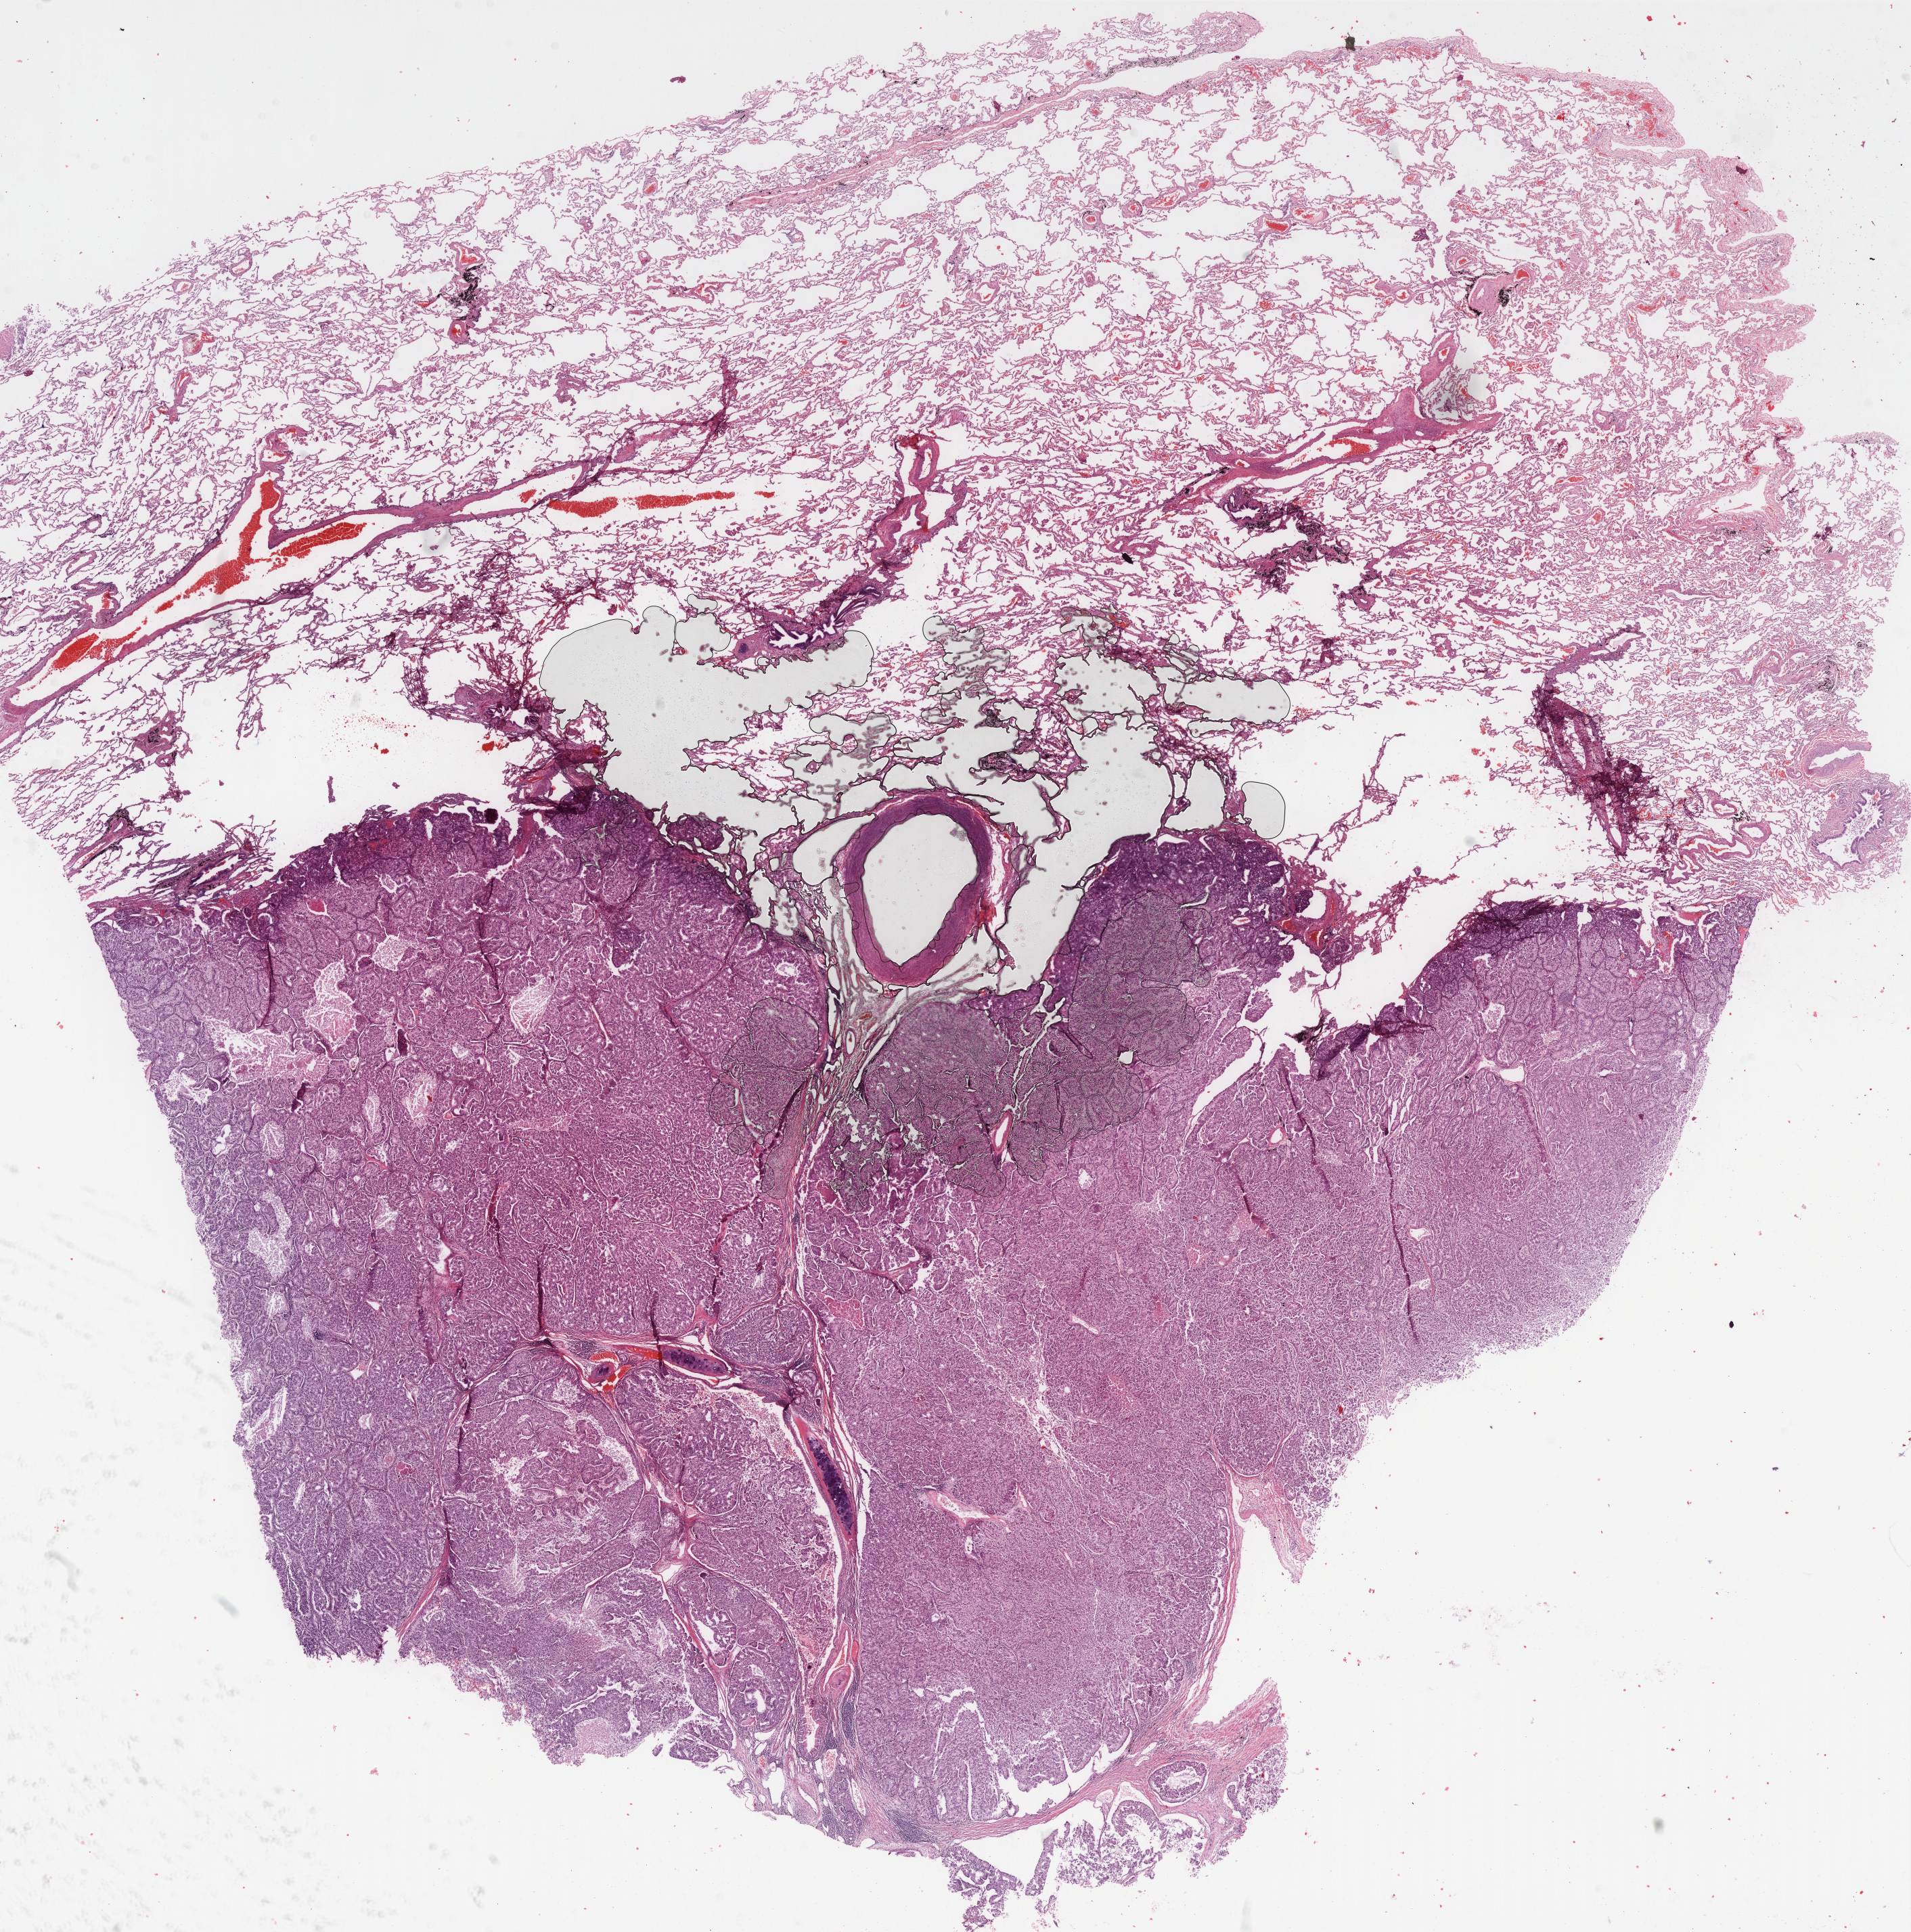
Digitized H&E tissue section (whole slide), low-resolution overview of the scanned area, about 22.7 x 23.0 mm (slide scanned at 40x). Formalin-fixed paraffin-embedded (FFPE) diagnostic section. Sample: primary tumour, lung. Male, age 84 years at initial diagnosis.
Diagnosis: Acinar cell carcinoma (upper lobe, lung). Laterality: right. TNM: T2 N0 M0. AJCC pathologic stage: IB (6th edition).